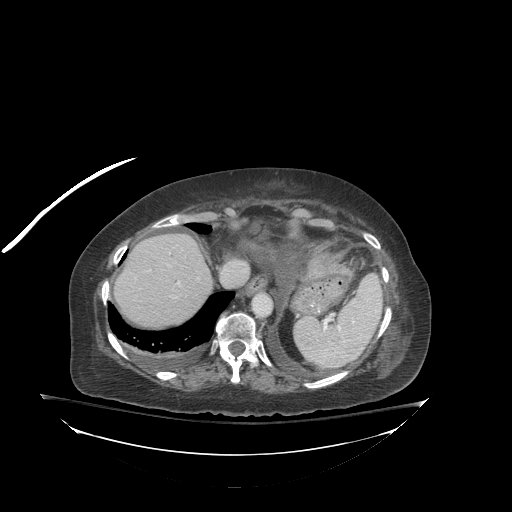
Contrast-enhanced abdominal CT (liver protocol), one axial slice. Position 70 of 81 along the scan axis. Reconstruction kernel STANDARD. 140 kVp. Soft-tissue window (W 400 / L 40 HU). 512 × 512 image matrix, field of view 500 × 500 mm. Case-level facts recorded for this patient, not image findings: diagnosis: hepatocellular carcinoma (patient treated with transarterial chemoembolisation; whether this scan precedes or follows treatment is not stated here); TNM stage (as recorded): Stage-I; Child-Pugh class: B; tumour differentiation: well-moderately differentiated; tumour nodularity: uninodular.
Outlined on this slice (semi-automatically segmented with operator editing):
- abdominal aorta: bounding box <253,295,272,317> (left, top, right, bottom; pixels)
- liver parenchyma outside the tumour (the mass and vessels are separate outlines, so this box may not span the whole liver): <123,234,212,324>
- liver vessels: <177,282,180,285>